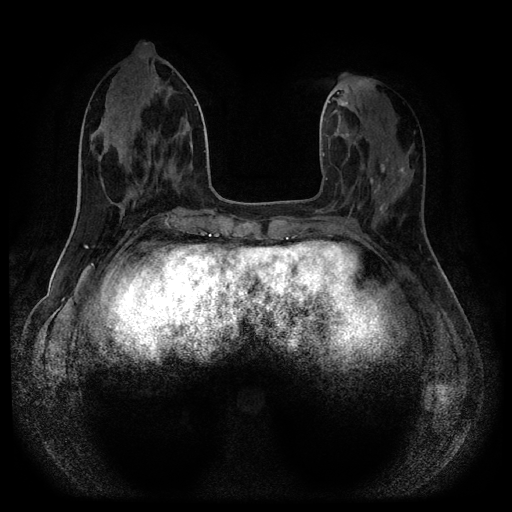
Breast MRI (dynamic contrast-enhanced, multi-phase), one axial slice. Slice 41 of 116 in the series (ordered by position). Dynamic contrast-enhanced series, time point 2 of 5 at this slice position (early post-contrast). 1.5 T. TE 2.7 ms, TR 5.4 ms. 512 × 512 image matrix. Female patient, age 40 years.
Annotated regions visible in this slice (semi-automatic segmentation, software-assisted and operator-edited):
- breast lesion (labelled benign in the annotation): bounding box [x1, y1, x2, y2] px = [337, 98, 349, 108]